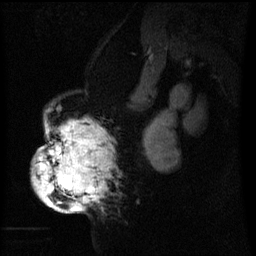
Breast MRI (dynamic contrast-enhanced), one sagittal slice. Position 37 of 60 along the scan axis. Dynamic contrast-enhanced series, image 2 of 3 at this slice position (ordered by acquisition). 1.5 T. TE 4.2 ms, TR 8 ms. 2.2 mm slice thickness. 256 × 256 image matrix, field of view 200 × 200 mm. Female patient, age 50 years.
Outlined on this slice (semi-automatic segmentation, software-assisted and operator-edited):
- analysis volume of interest (the breast-tissue region the enhancement analysis was run in; not a lesion): bounding box <34,118,111,211> (left, top, right, bottom; pixels)
- tumour enhancement mask (voxels above the 70 % enhancement threshold inside the analysis volume of interest): <35,122,105,211>